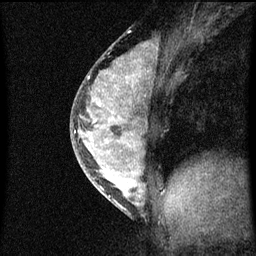
Breast MRI (dynamic contrast-enhanced), one sagittal slice. Position 31 of 60 along the scan axis. Dynamic contrast-enhanced series, image 2 of 3 at this slice position (ordered by acquisition). 1.5 T. TE 4.2 ms, TR 8 ms. 256 × 256 image matrix. Patient: female, 33 years.
Structures marked on this image (semi-automatically segmented with operator editing):
- analysis volume of interest (the breast-tissue region the enhancement analysis was run in; not a lesion): box from (x=71, y=56) to (x=159, y=215) px
- tumour enhancement mask (voxels above the 70 % enhancement threshold inside the analysis volume of interest): (x=75, y=60)–(x=145, y=205)